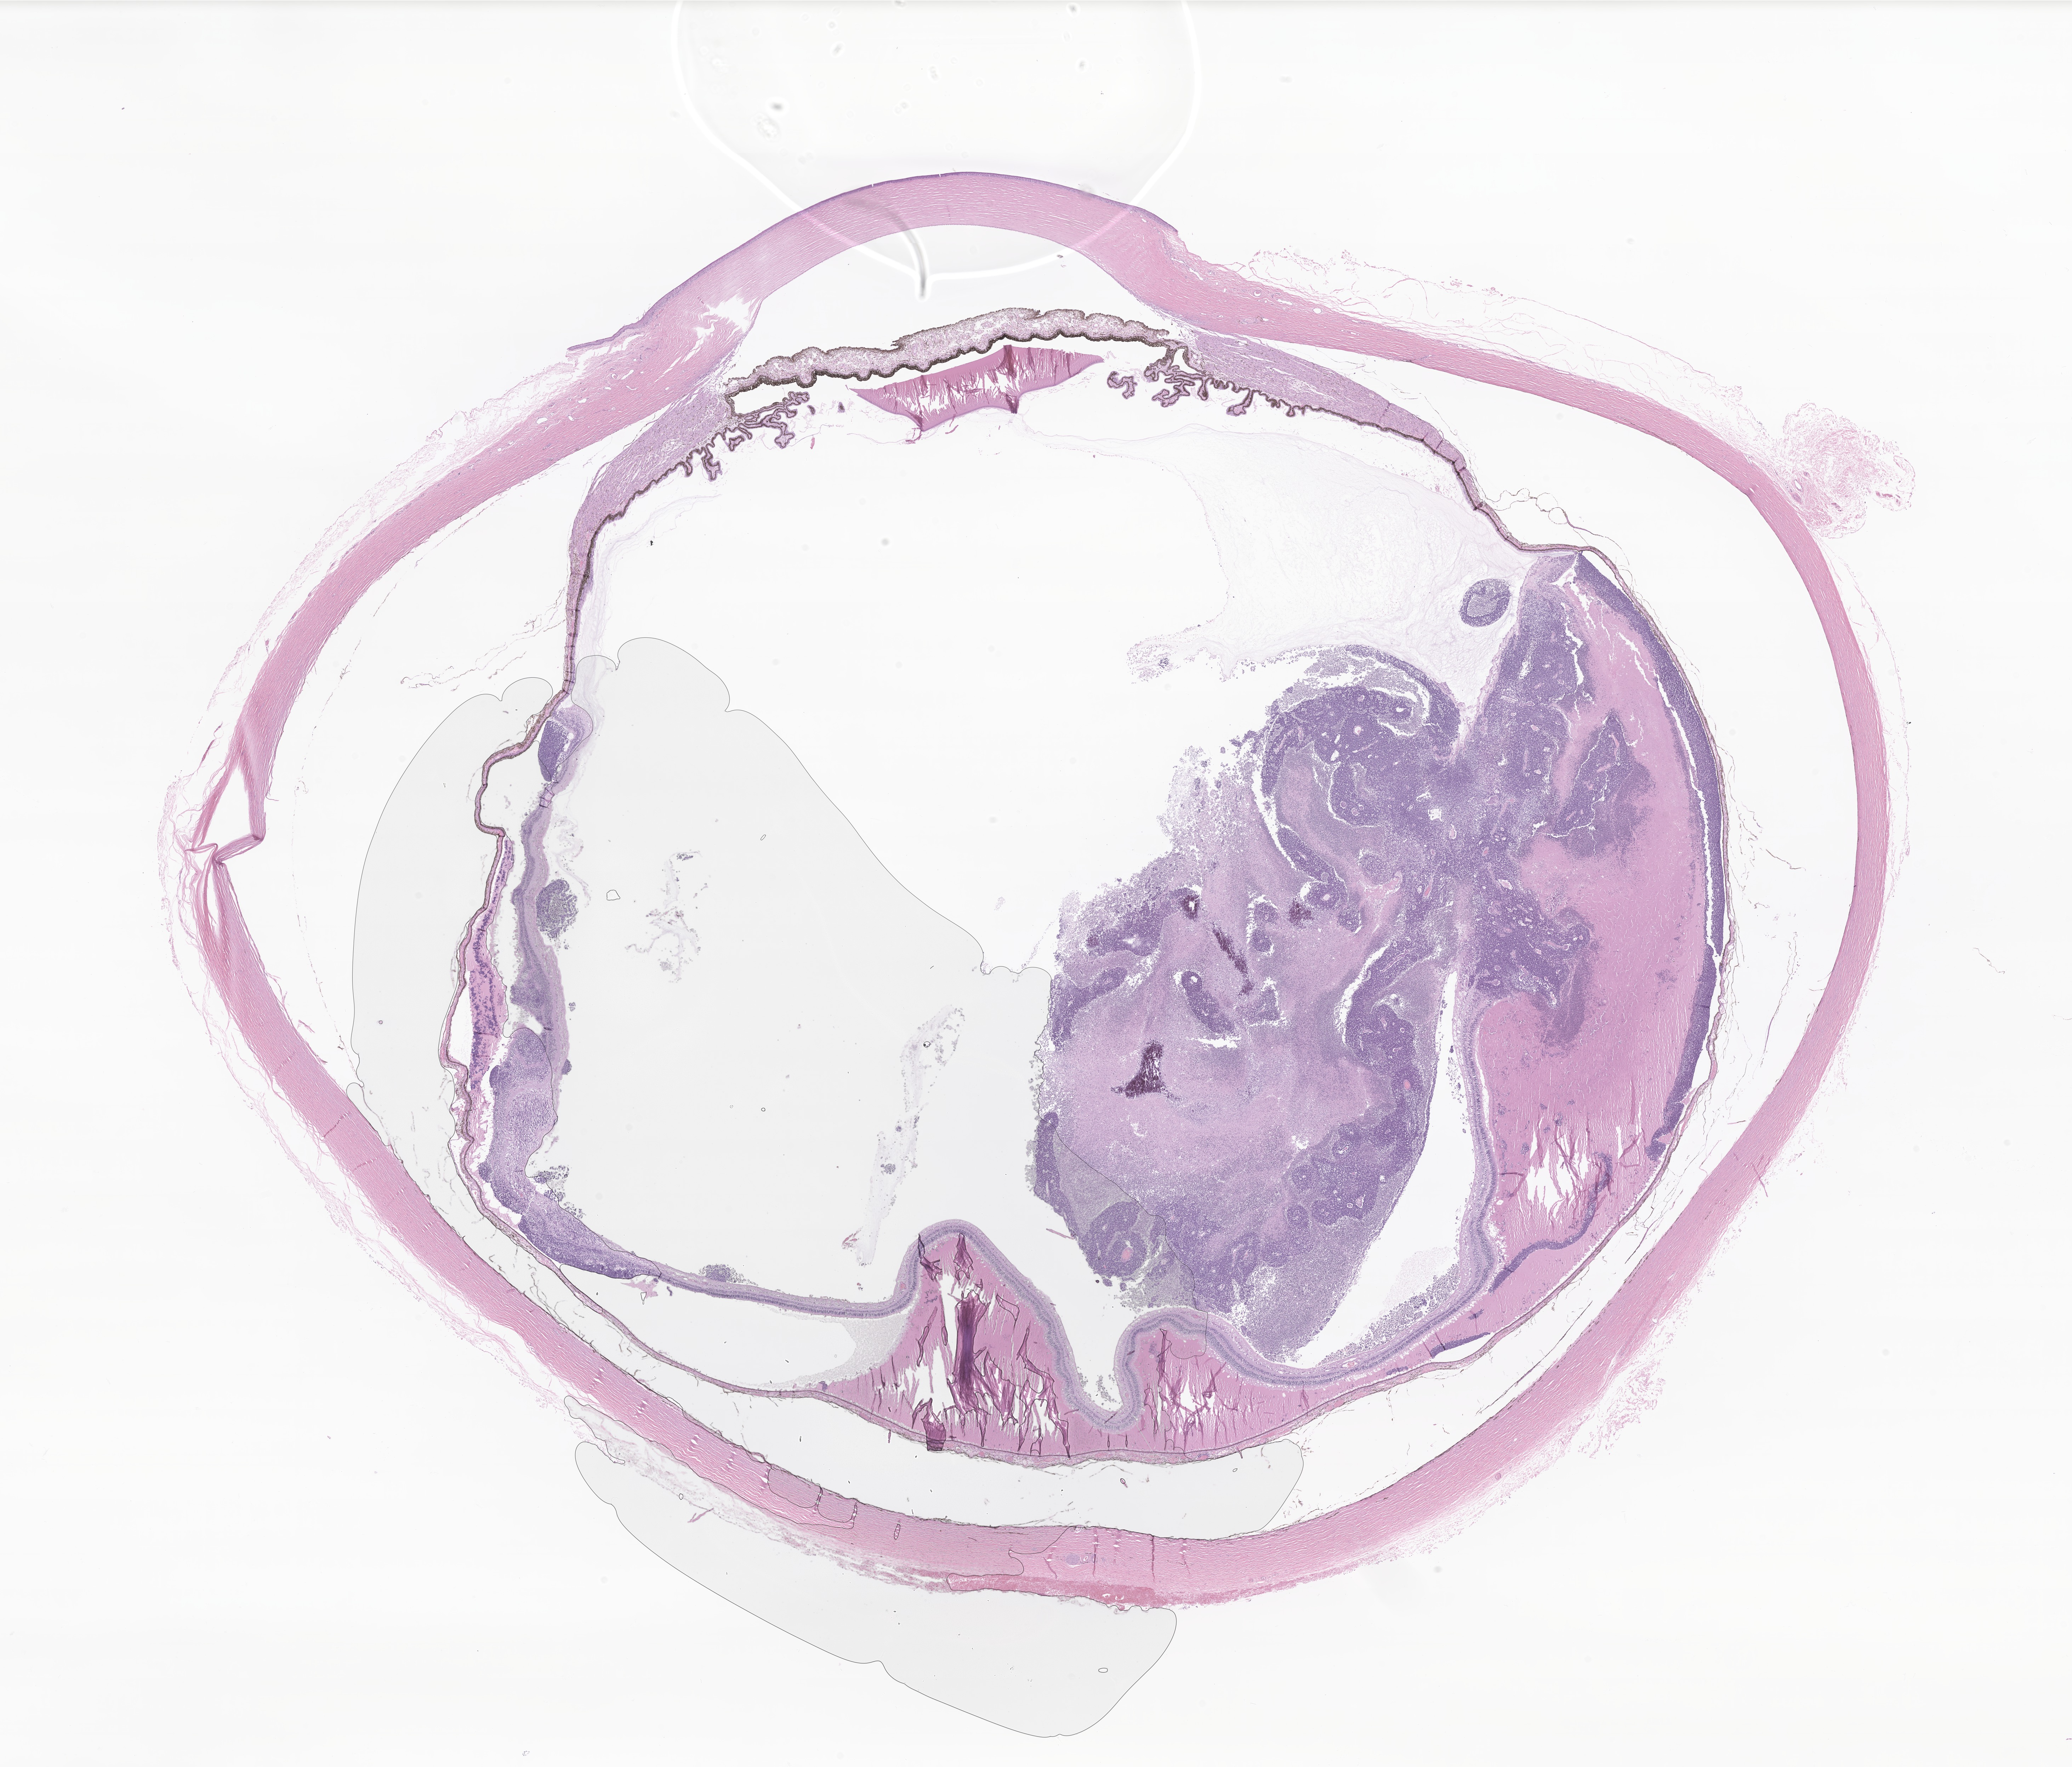
Digitized H&E-stained section of tumor tissue from the orbit — a low-resolution overview of the entire scanned area, about 24.7 x 21.0 mm, formalin-fixed, paraffin-embedded (FFPE) tissue. Patient: female, age 34 months (2 years 10 months).
Recorded diagnosis: Retinoblastoma, NOS.